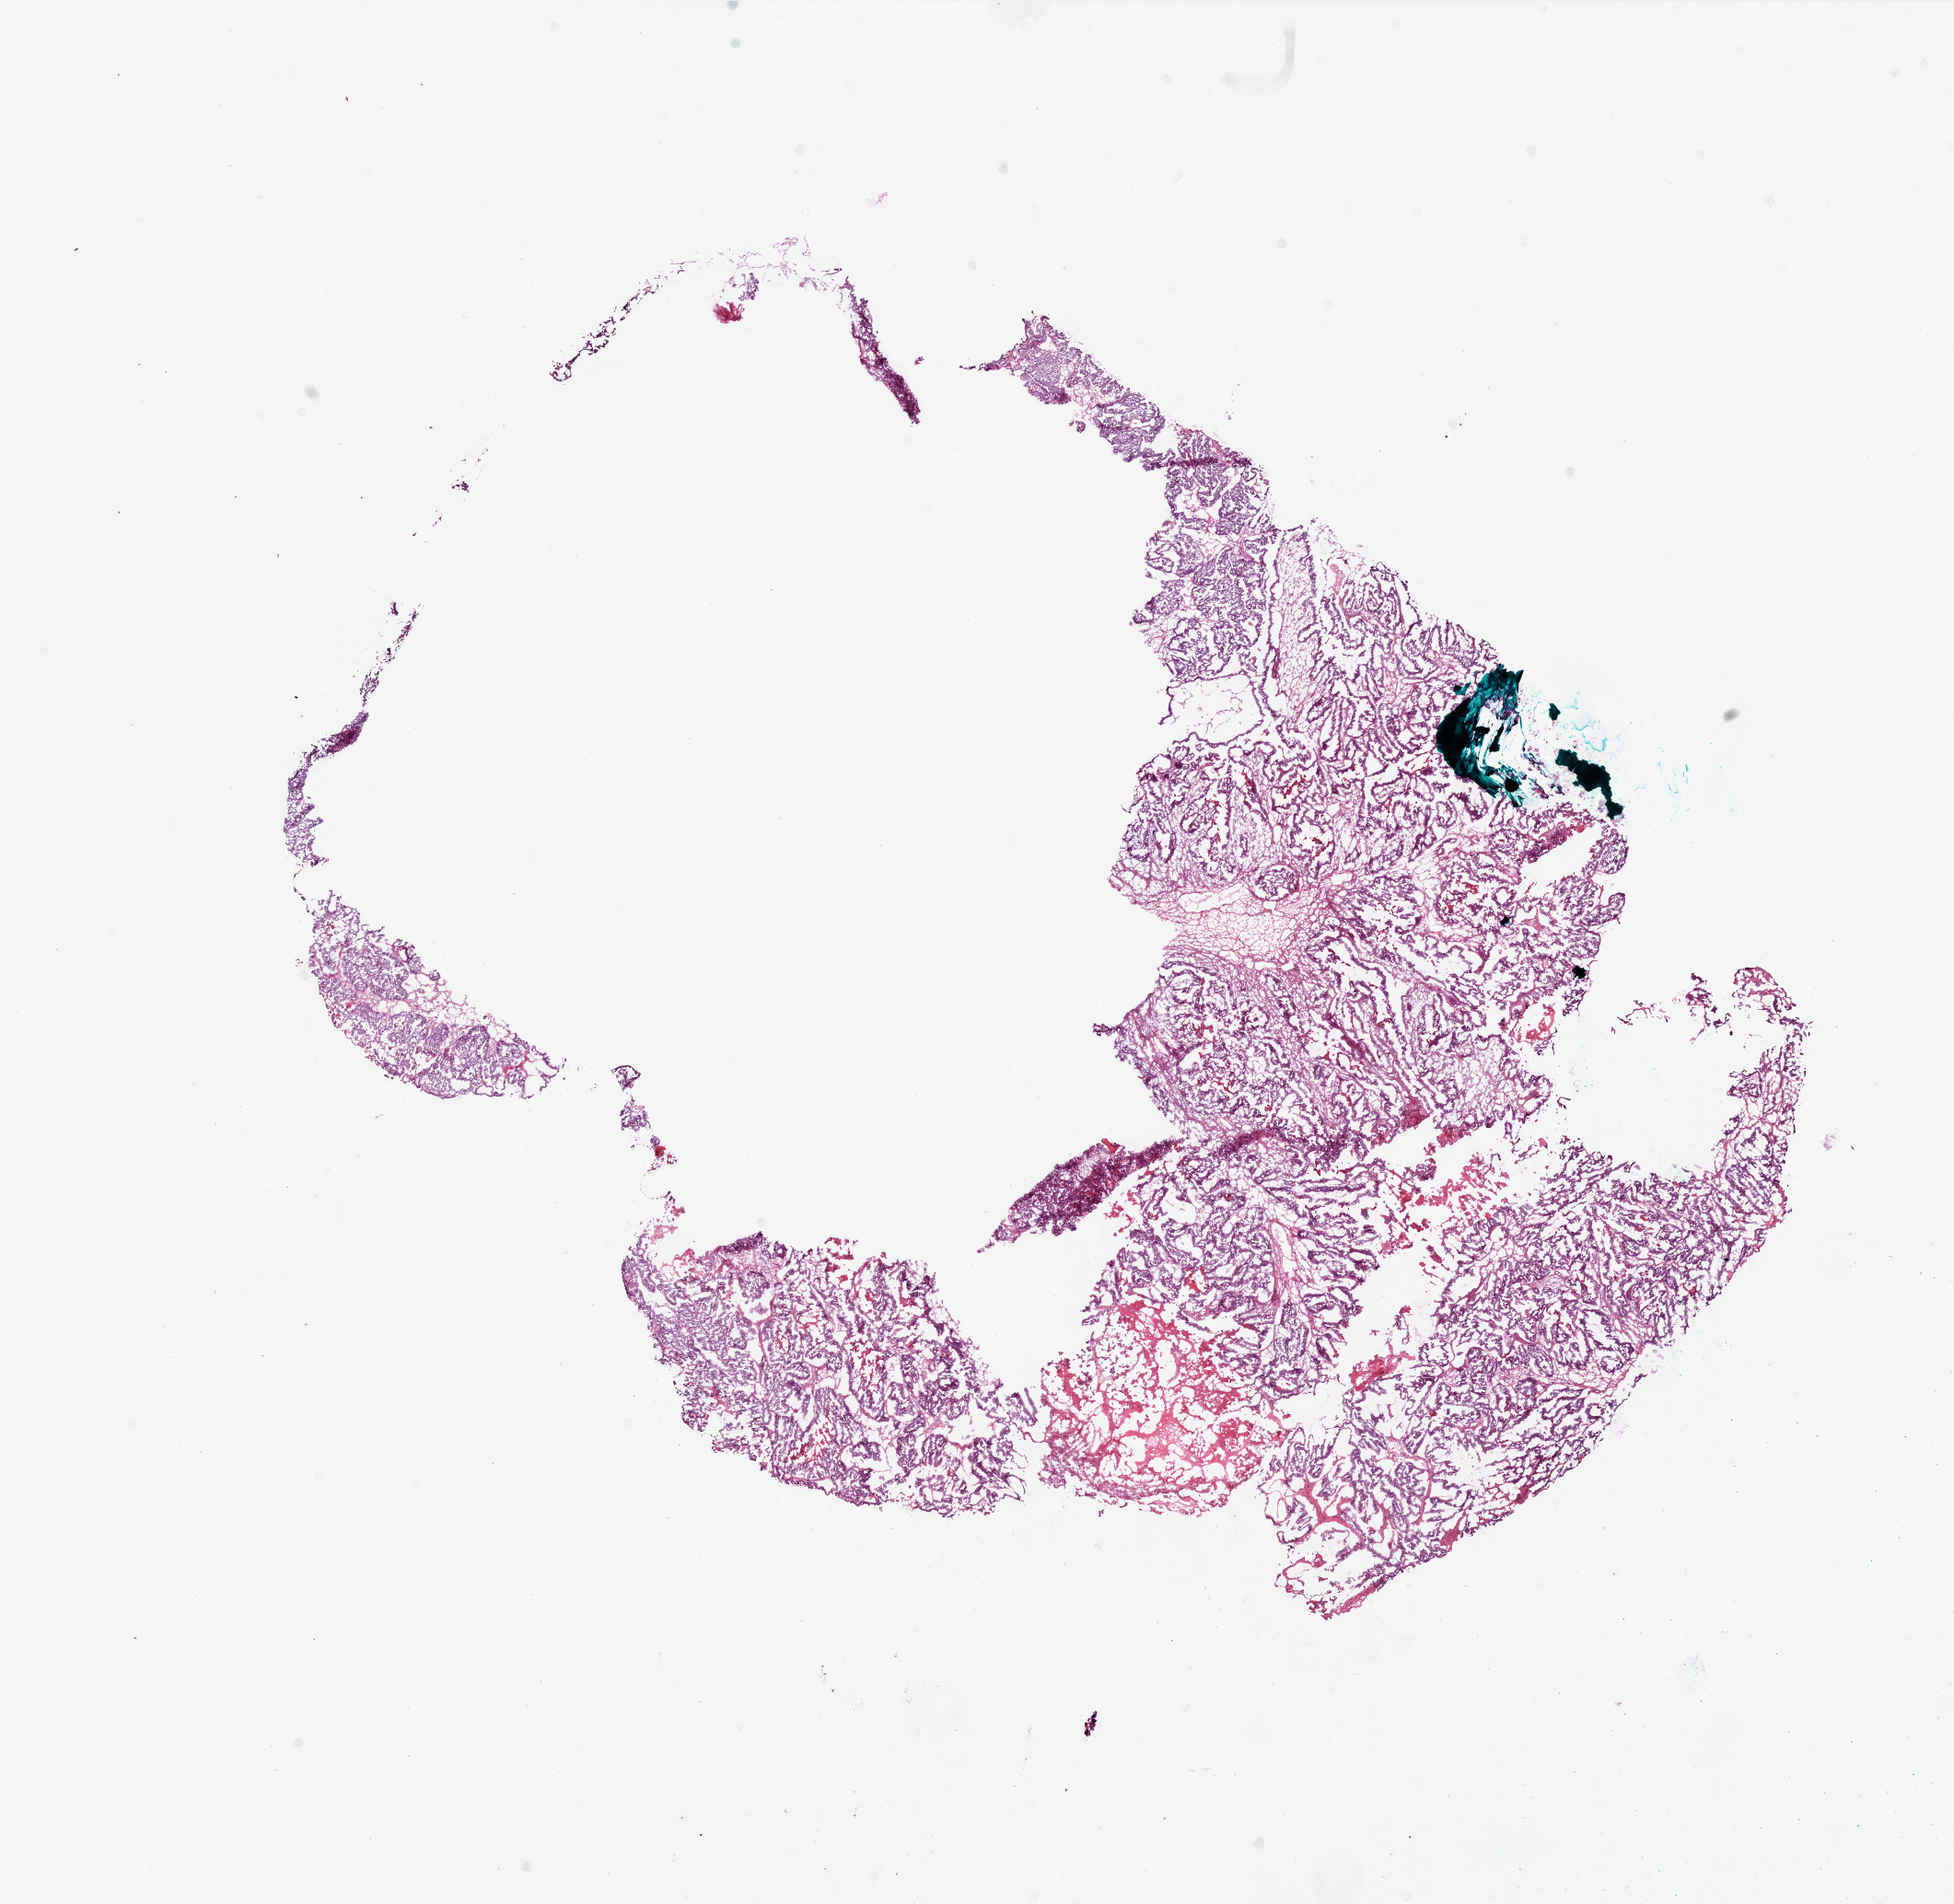
Hematoxylin and eosin (H&E) stained whole-slide image — low-resolution overview of the scanned area, about 17.0 x 16.6 mm. Slide review estimates, as recorded: tumour cells 85%, tumour nuclei 90%, stromal cells 10%, necrosis 5%.
Specimen: frozen section; ovary, primary tumour sample.